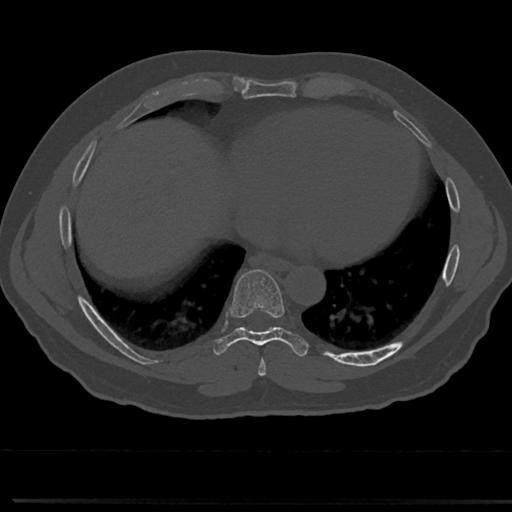
CT including the spine, one axial slice. Position 355 of 817 along the scan axis. Reconstruction kernel Br40s/3. 120 kVp. Bone window (W 1800 / L 400 HU). 0.5 mm slice thickness. 512 × 512 image matrix, field of view 355 × 355 mm. Patient: male, 61 years. Case-level facts recorded for this patient, not image findings: primary cancer: prostate.
Annotated regions visible in this slice (semi-automatic segmentation, software-assisted and operator-edited):
- T7 vertebra: bounding box (x1, y1, x2, y2) in pixels: (241, 330, 282, 363)
- T8 vertebra: (236, 270, 284, 335)